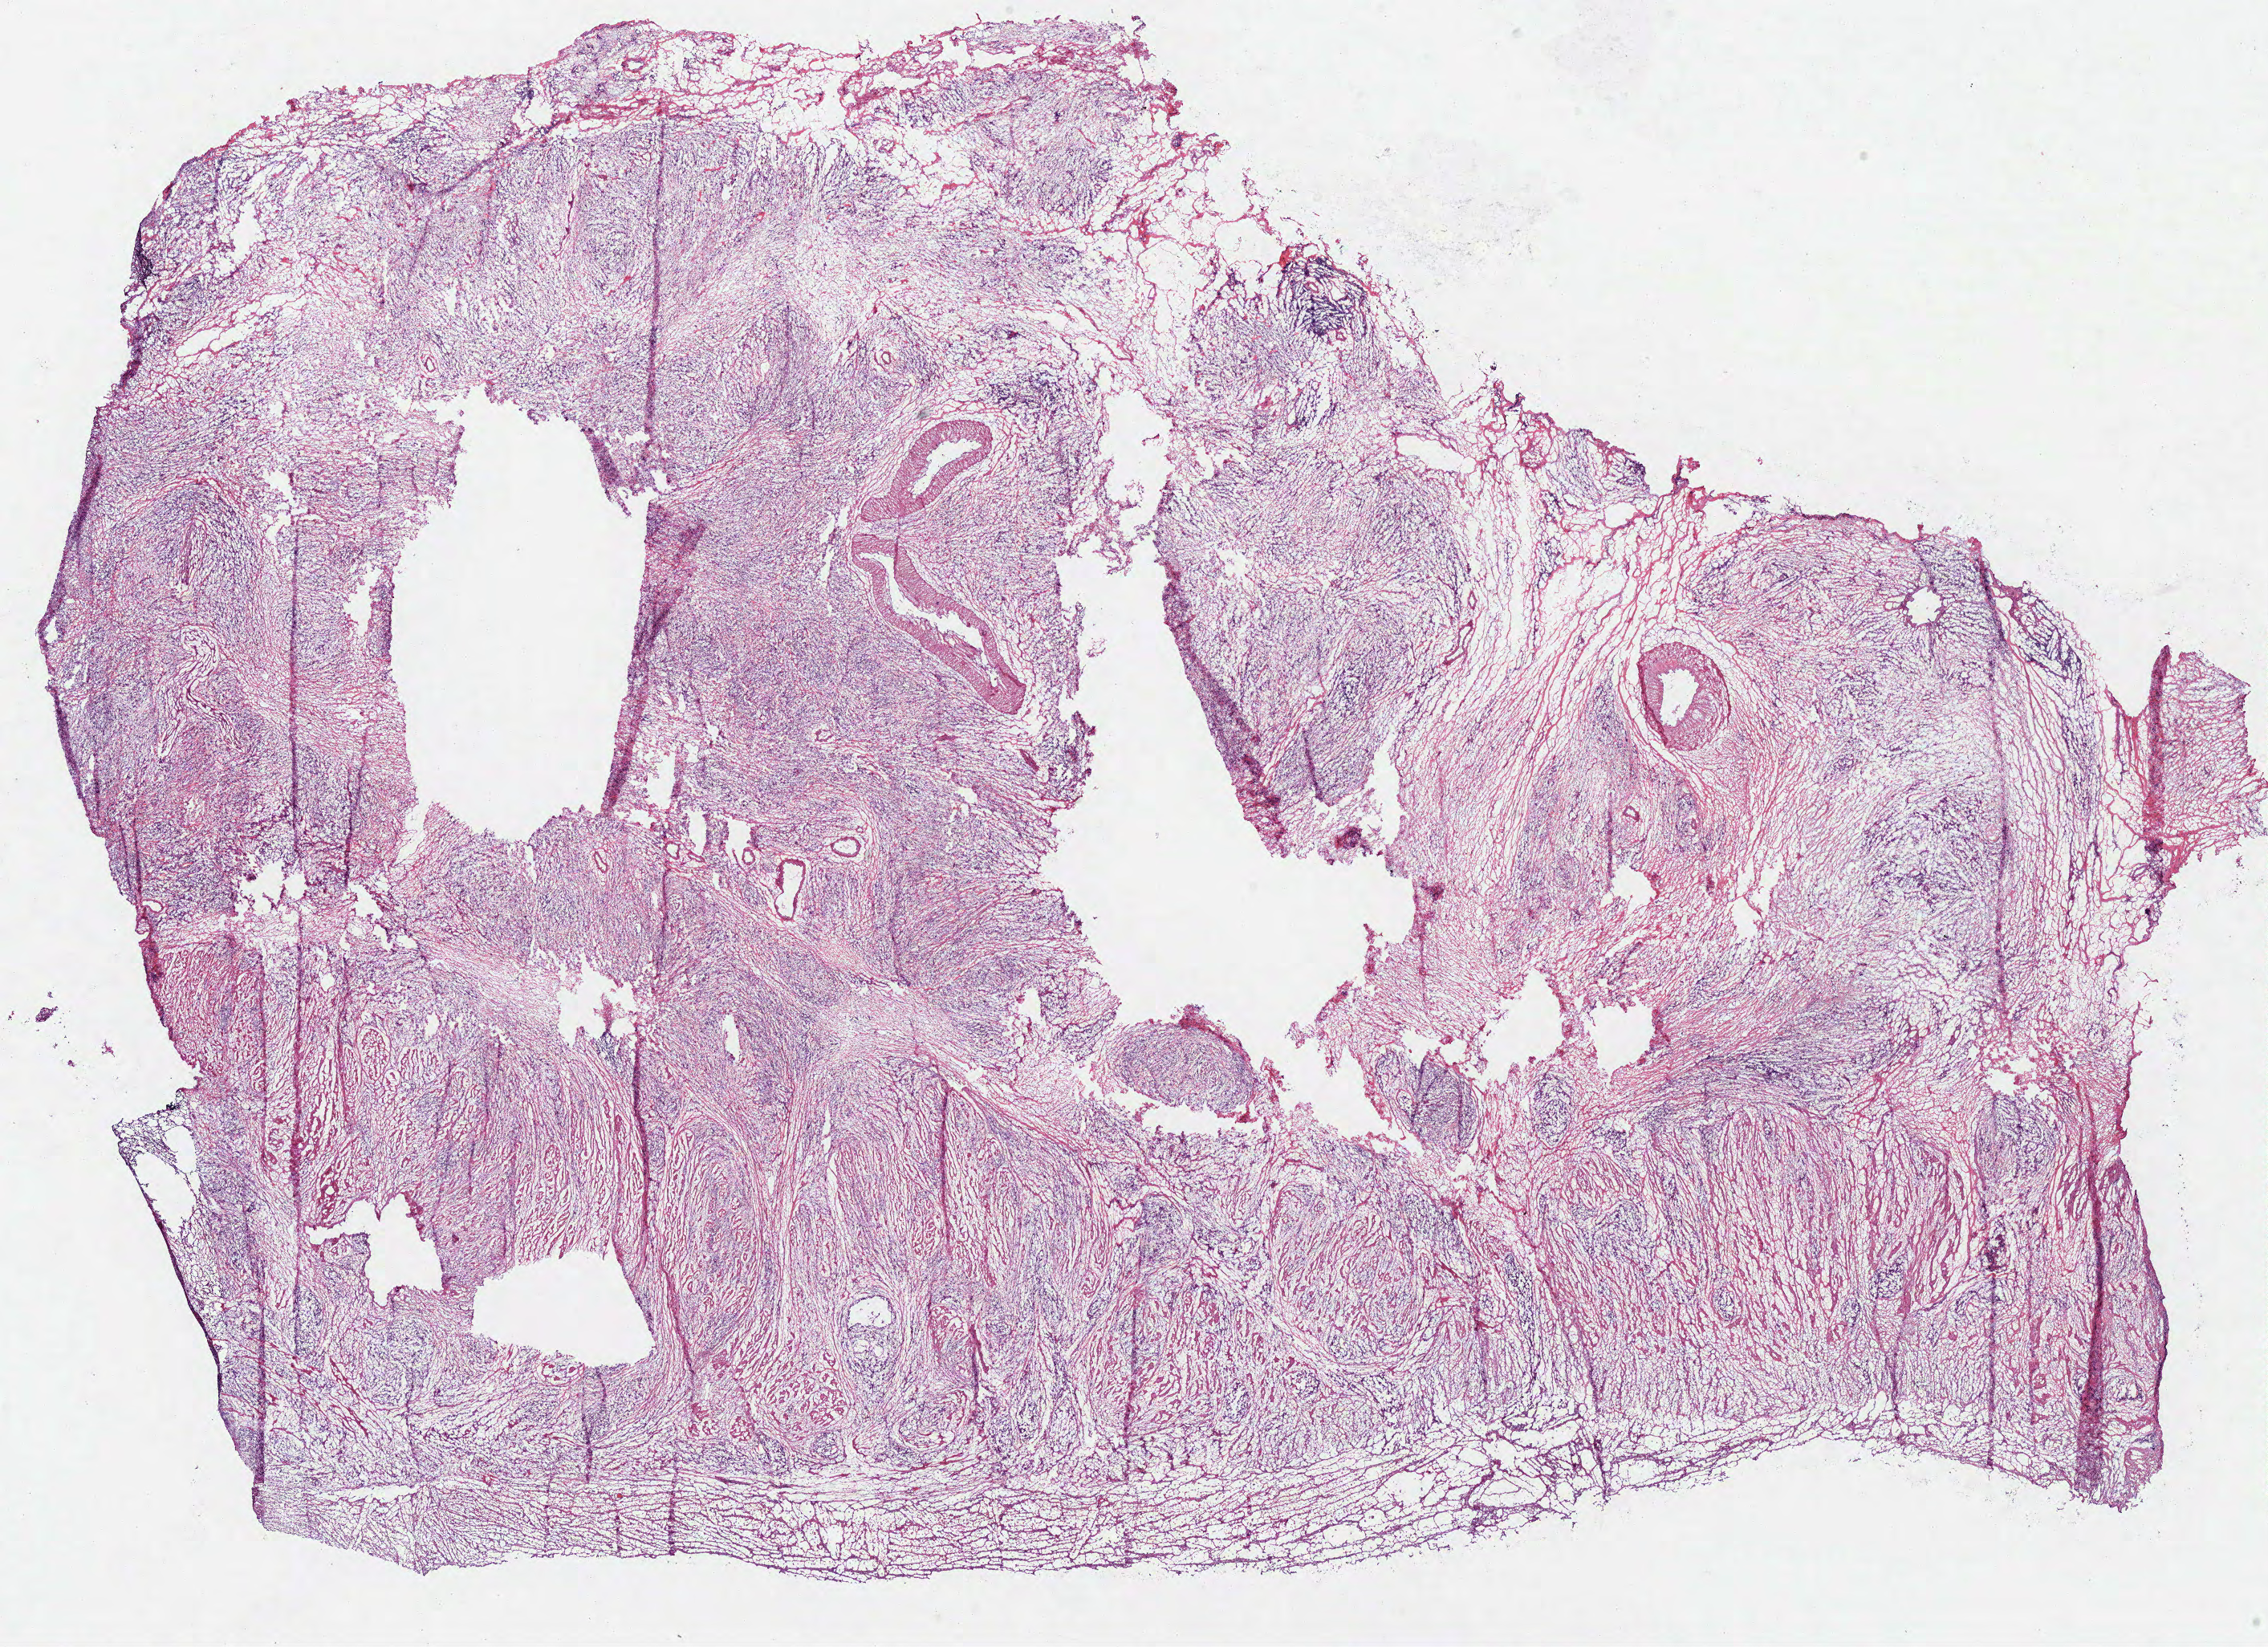
Whole-slide histology image, Hematoxylin and eosin (H&E) stained — a low-resolution overview of the entire scanned area, about 22.3 x 16.2 mm (slide scanned at 40x). Frozen section from the bottom of the tissue portion. Primary tumour sample from the stomach. Patient: male, age at initial diagnosis 64 years.
Diagnosis: Adenocarcinoma, NOS (cardia, NOS).